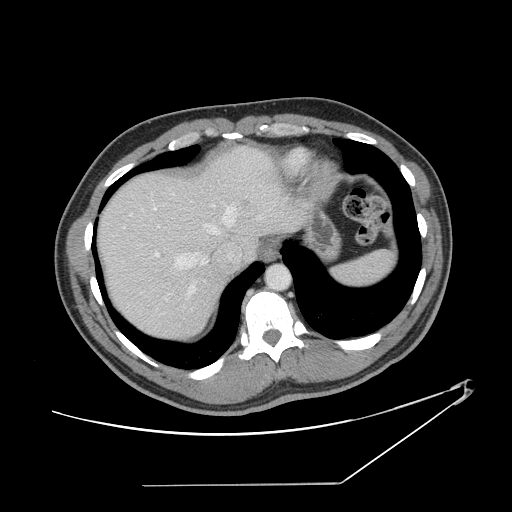
Contrast-enhanced abdominal CT, one axial slice; slice 122 of 152 in the series (ordered by position); 120 kVp; intravenous contrast given; soft-tissue window (W 400 / L 40 HU); 2.5 mm slice thickness; 512 × 512 image matrix. Male patient, age 45 years. Case-level facts recorded for this patient, not image findings: diagnosis: colorectal cancer liver metastases, imaged before liver resection; multiple liver metastases: no; largest metastasis: 1 cm; disease in both lobes: no.
Outlined on this slice (outlined manually by an expert reader):
- hepatic veins: box from (x=123, y=203) to (x=237, y=299) px
- liver: (x=100, y=149)–(x=297, y=339)
- planned liver remnant (the part of the liver to remain after resection): (x=101, y=175)–(x=234, y=339)
- portal vein (with intrahepatic branches): (x=155, y=253)–(x=192, y=310)
- liver metastasis: (x=243, y=202)–(x=250, y=209)